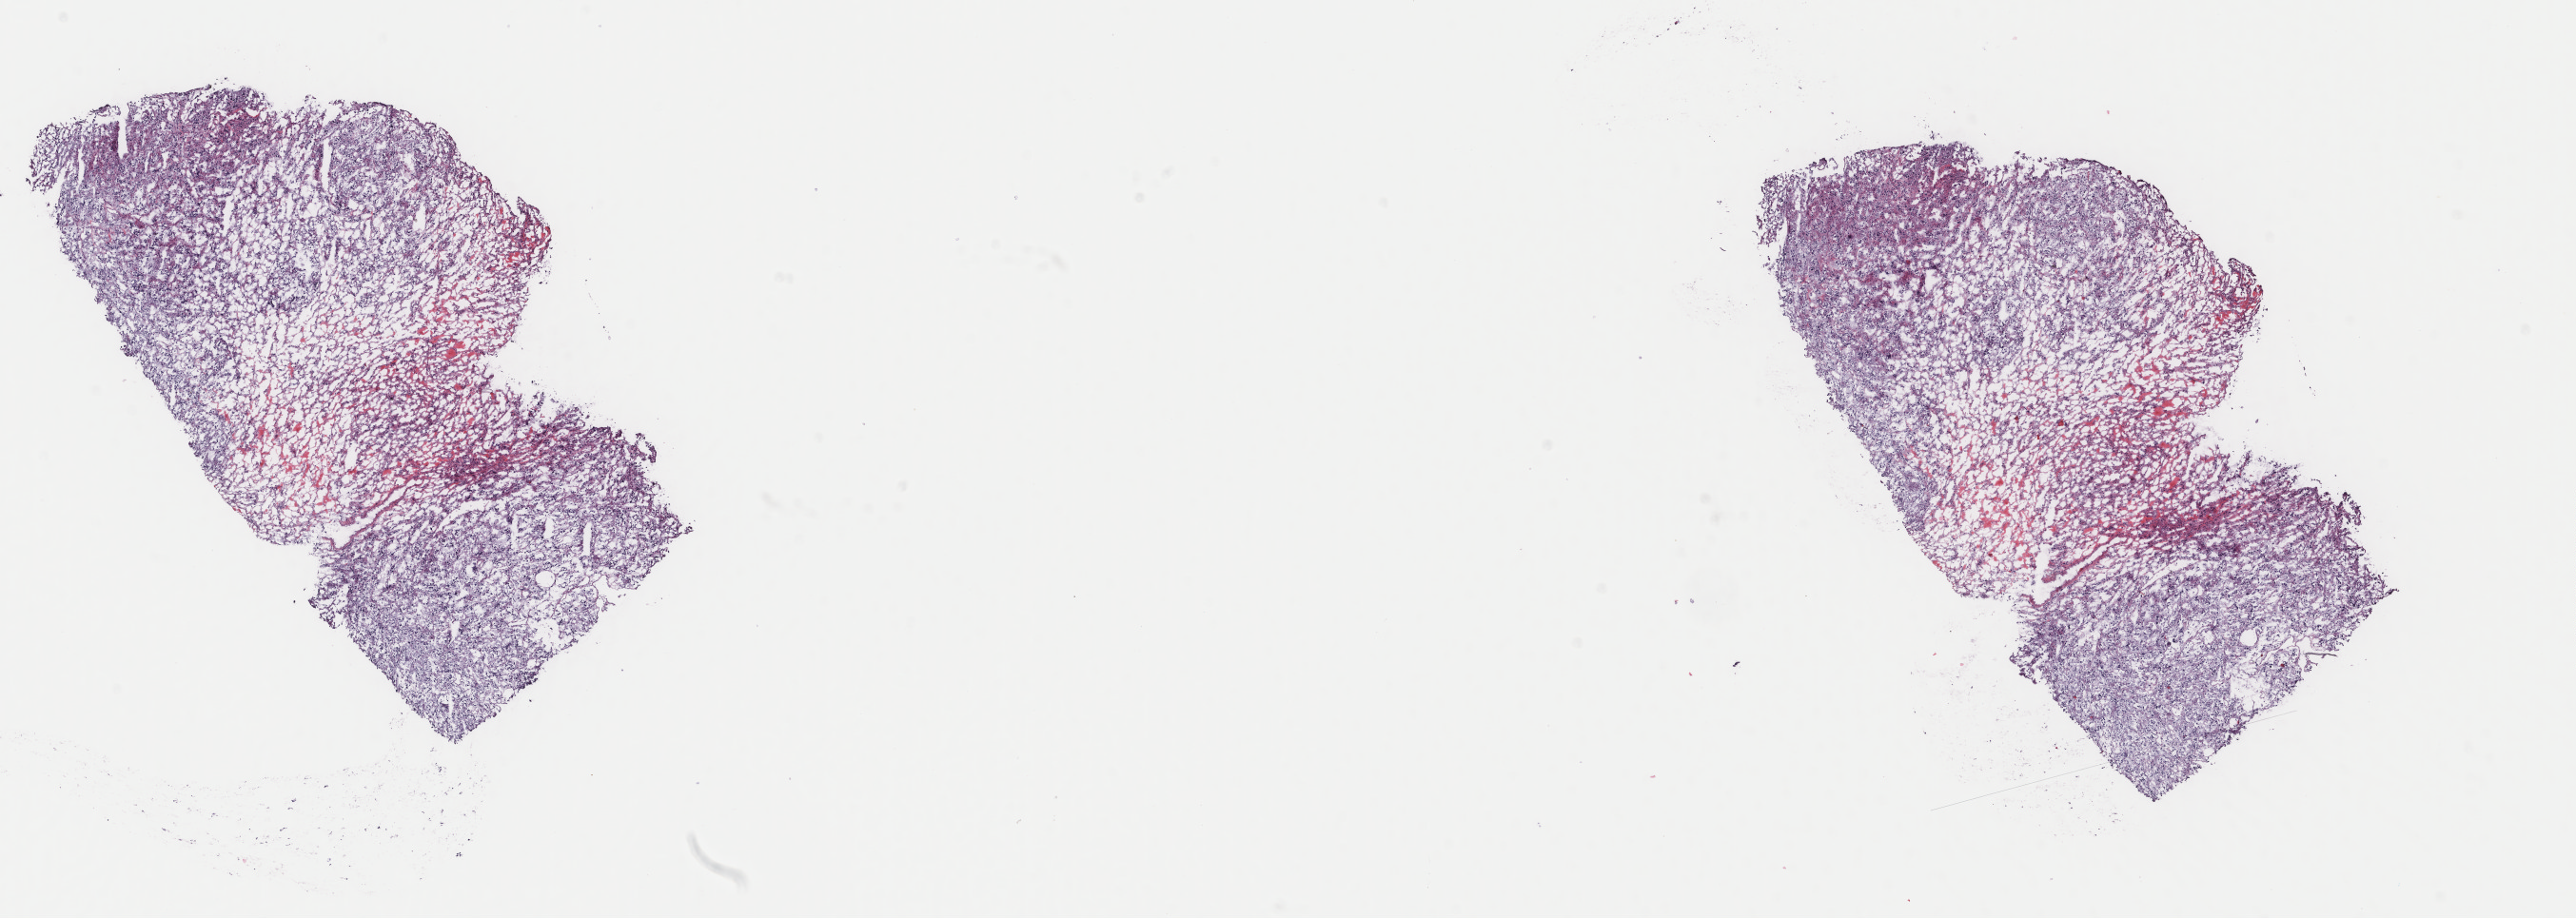
Whole-slide histology image, H&E-stained, shown as a low-resolution overview of the whole scanned area (about 21.5 x 7.7 mm, acquisition: 40x scan), frozen section, sample: primary tumour, adrenal gland. Male, age 31 years at initial diagnosis. Composition of this section per pathologist review: tumour cells 90%, tumour nuclei 95%, normal cells 0%, stromal cells 10%, necrosis 0%. Inflammatory infiltration, as recorded: lymphocyte infiltration 0%, monocyte infiltration 0%, neutrophil infiltration 0%.
Pathologic diagnosis: Pheochromocytoma, NOS. Laterality: right.